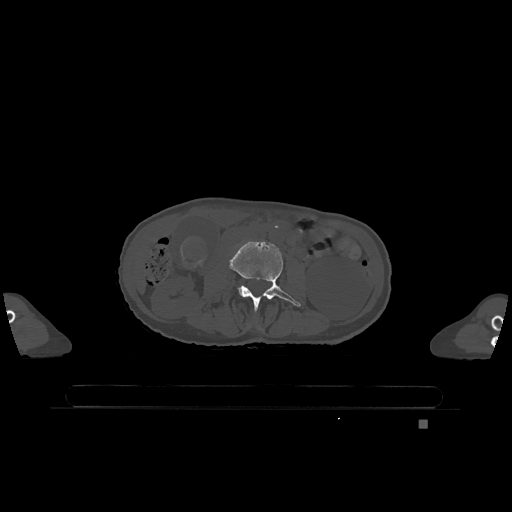
CT including the spine, one axial slice; position 355 of 1317 along the scan axis; bone window (W 1800 / L 400 HU); 0.5 mm slice thickness; 512 × 512 image matrix, field of view 500 × 500 mm. Female patient, age 74 years. Case-level facts recorded for this patient, not image findings: primary cancer: lung.
Outlined on this slice (semi-automatically segmented with operator editing):
- L3 vertebra: bounding box (x1, y1, x2, y2) in pixels: (230, 241, 301, 311)